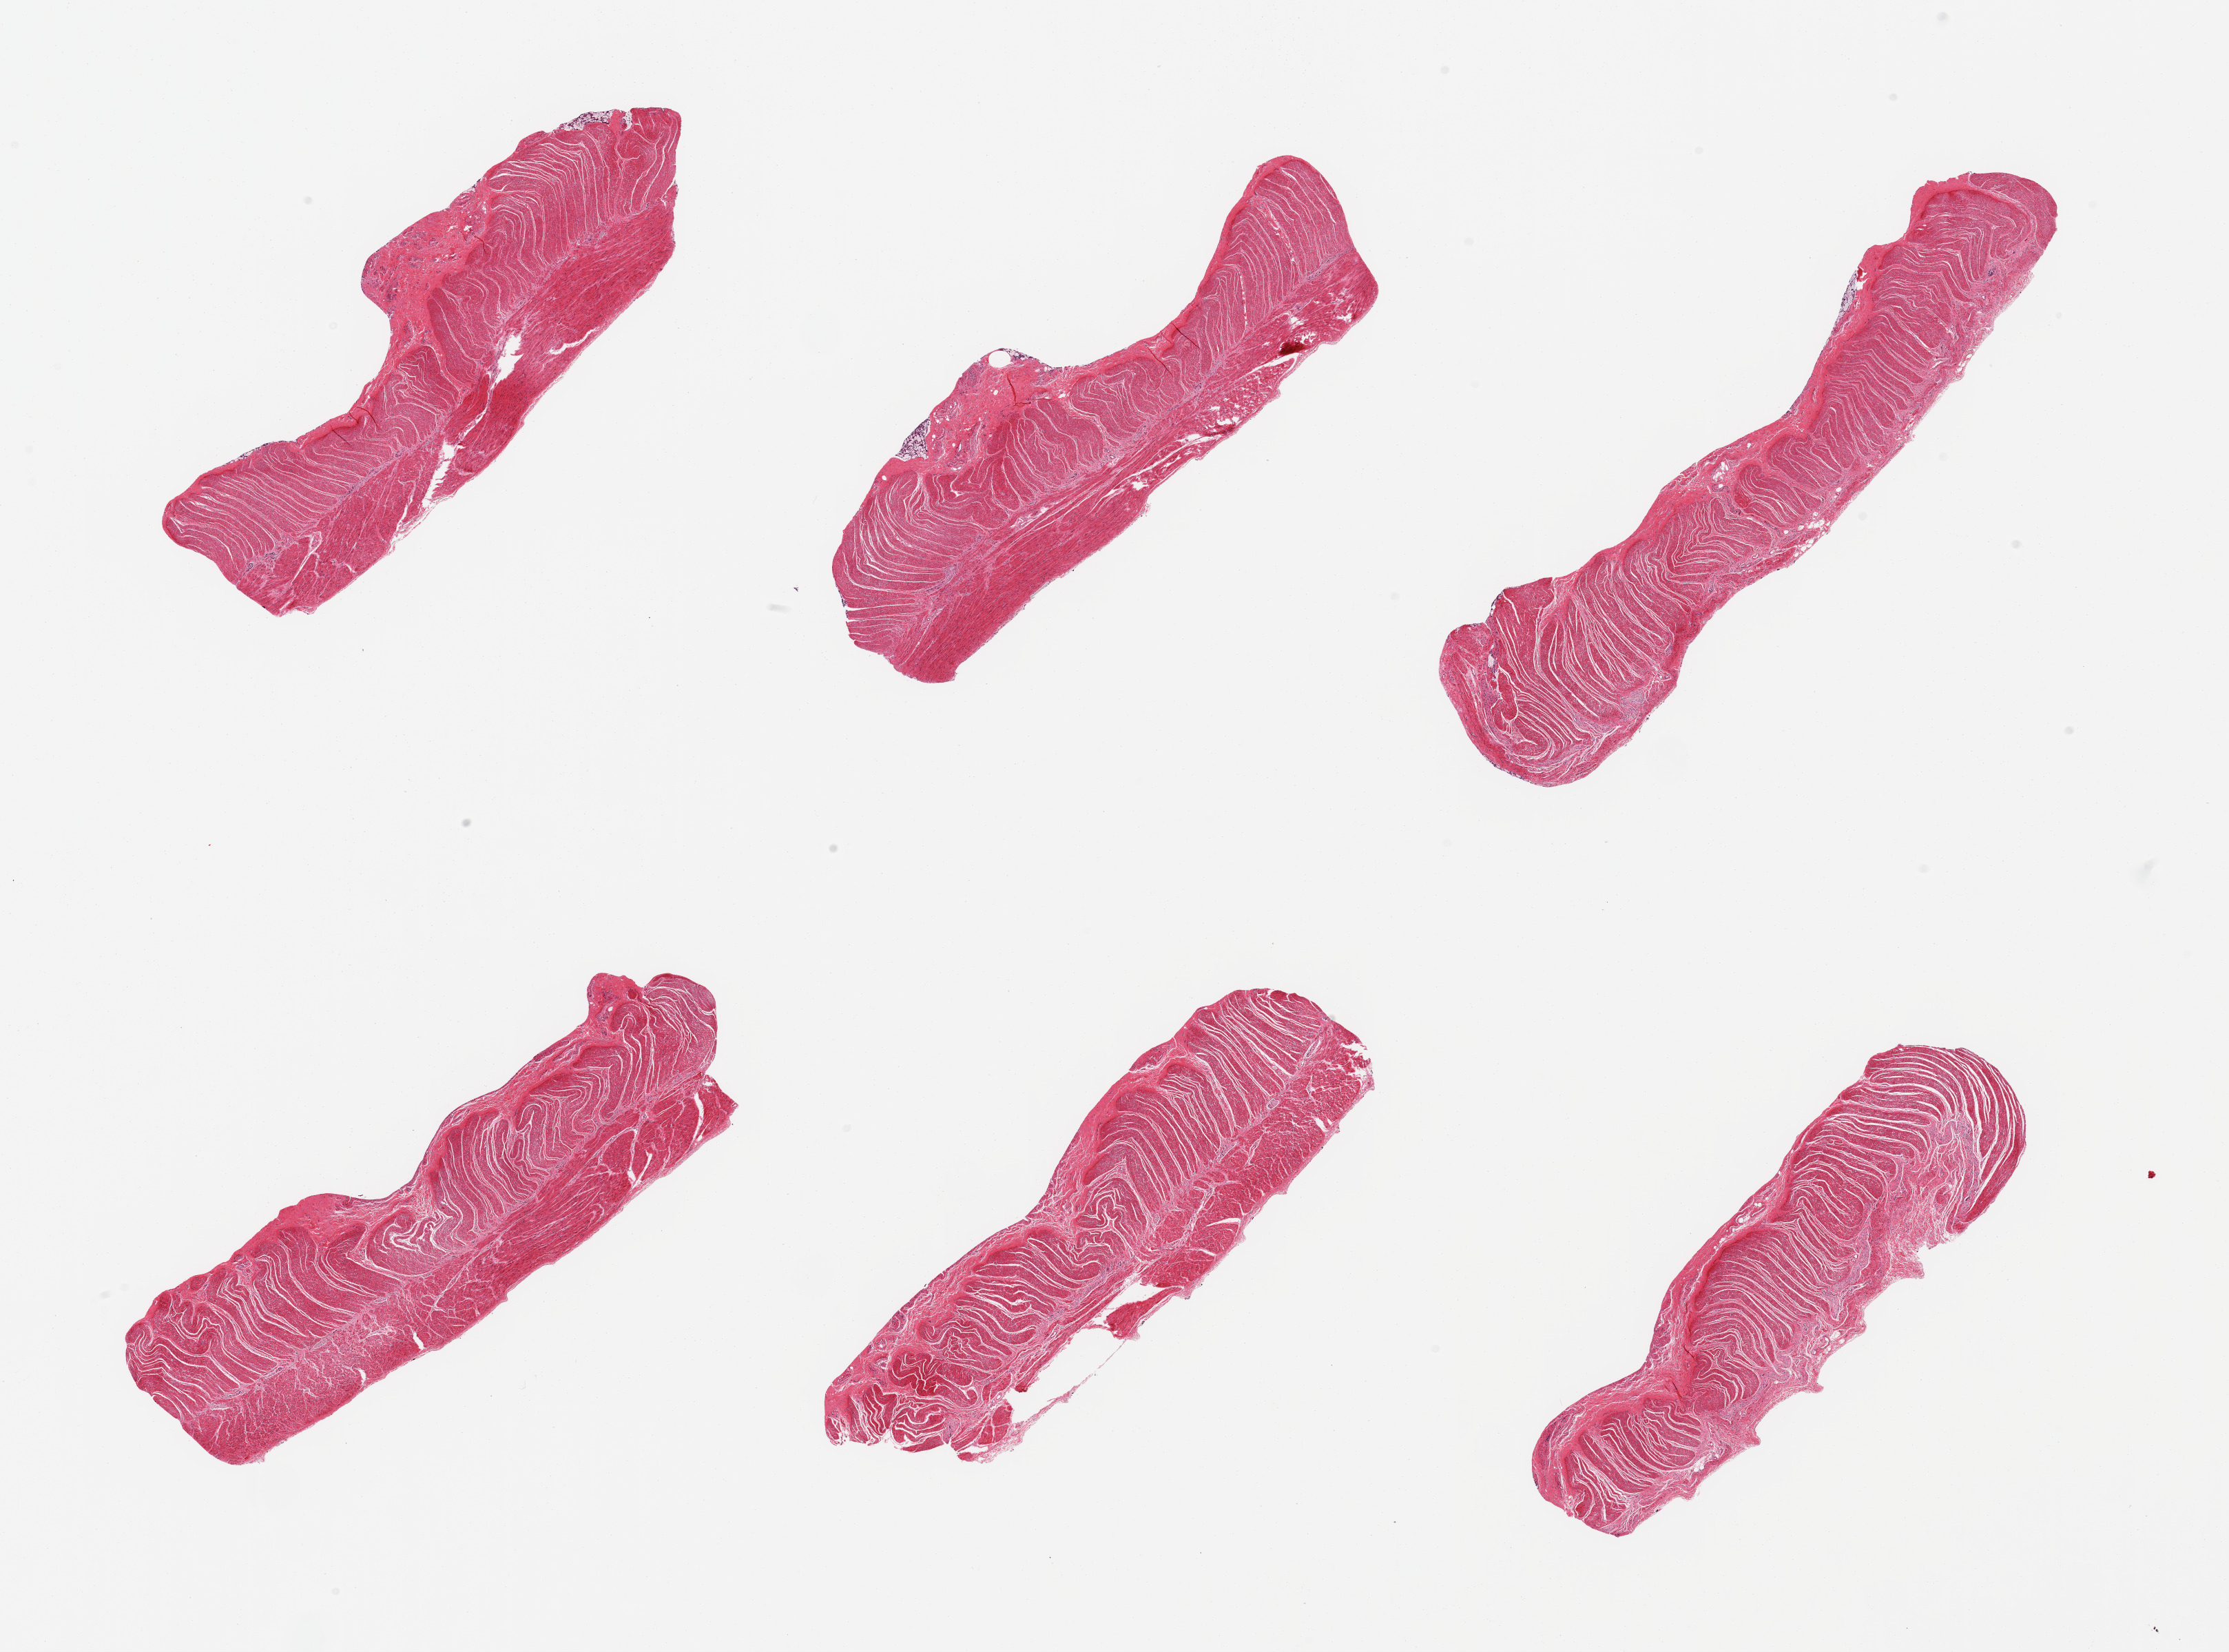
Digitized H&E-stained section, low-resolution overview of the scanned area, about 25.6 x 19.0 mm; PAXgene-fixed paraffin-embedded (PFPE) section; sampled site (target tissue): sigmoid colon; donor tissue sample. Donor sex: male.
Reviewer comment on this tissue sample: 6 pieces all musculars.